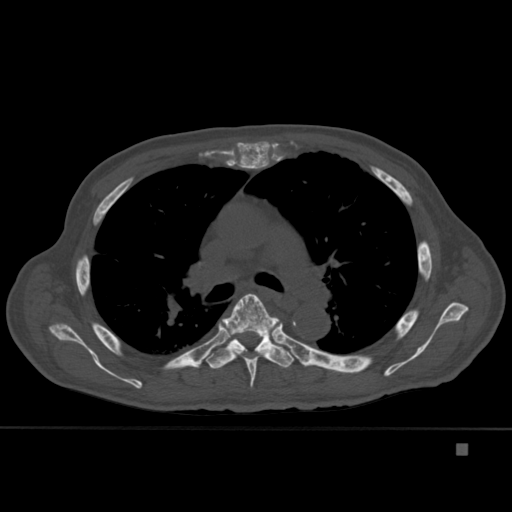
CT including the spine, one axial slice. Position 301 of 451 along the scan axis. Bone window (W 1800 / L 400 HU). 512 × 512 image matrix, field of view 378 × 378 mm. Patient: male, 75 years. From the clinical record (not read from this slice): primary cancer: prostate.
Annotated regions visible in this slice (semi-automatically segmented with operator editing):
- T5 vertebra: bounding box <218,293,282,388> (left, top, right, bottom; pixels)
- T6 vertebra: <205,328,294,369>